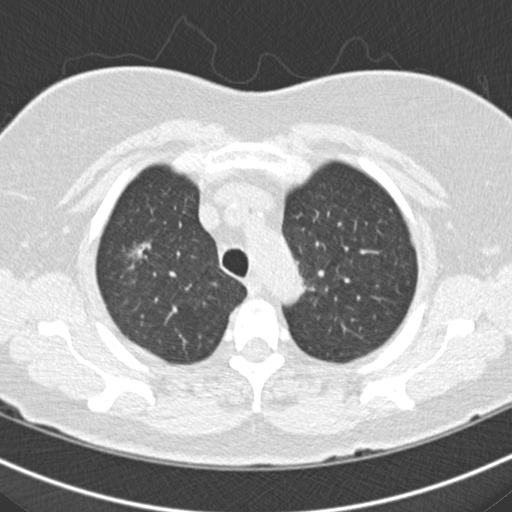
Low-dose screening chest CT, one axial slice. Position 137 of 160 along the scan axis. 120 kVp. Lung window (W 1500 / L -600 HU). 2 mm slice thickness. 512 × 512 image matrix, field of view 316 × 316 mm.
Annotated regions visible in this slice (expert manual segmentation):
- lesion 3 (nodule, upper lobe of right lung): bounding box (x1, y1, x2, y2) in pixels: (131, 244, 146, 261)